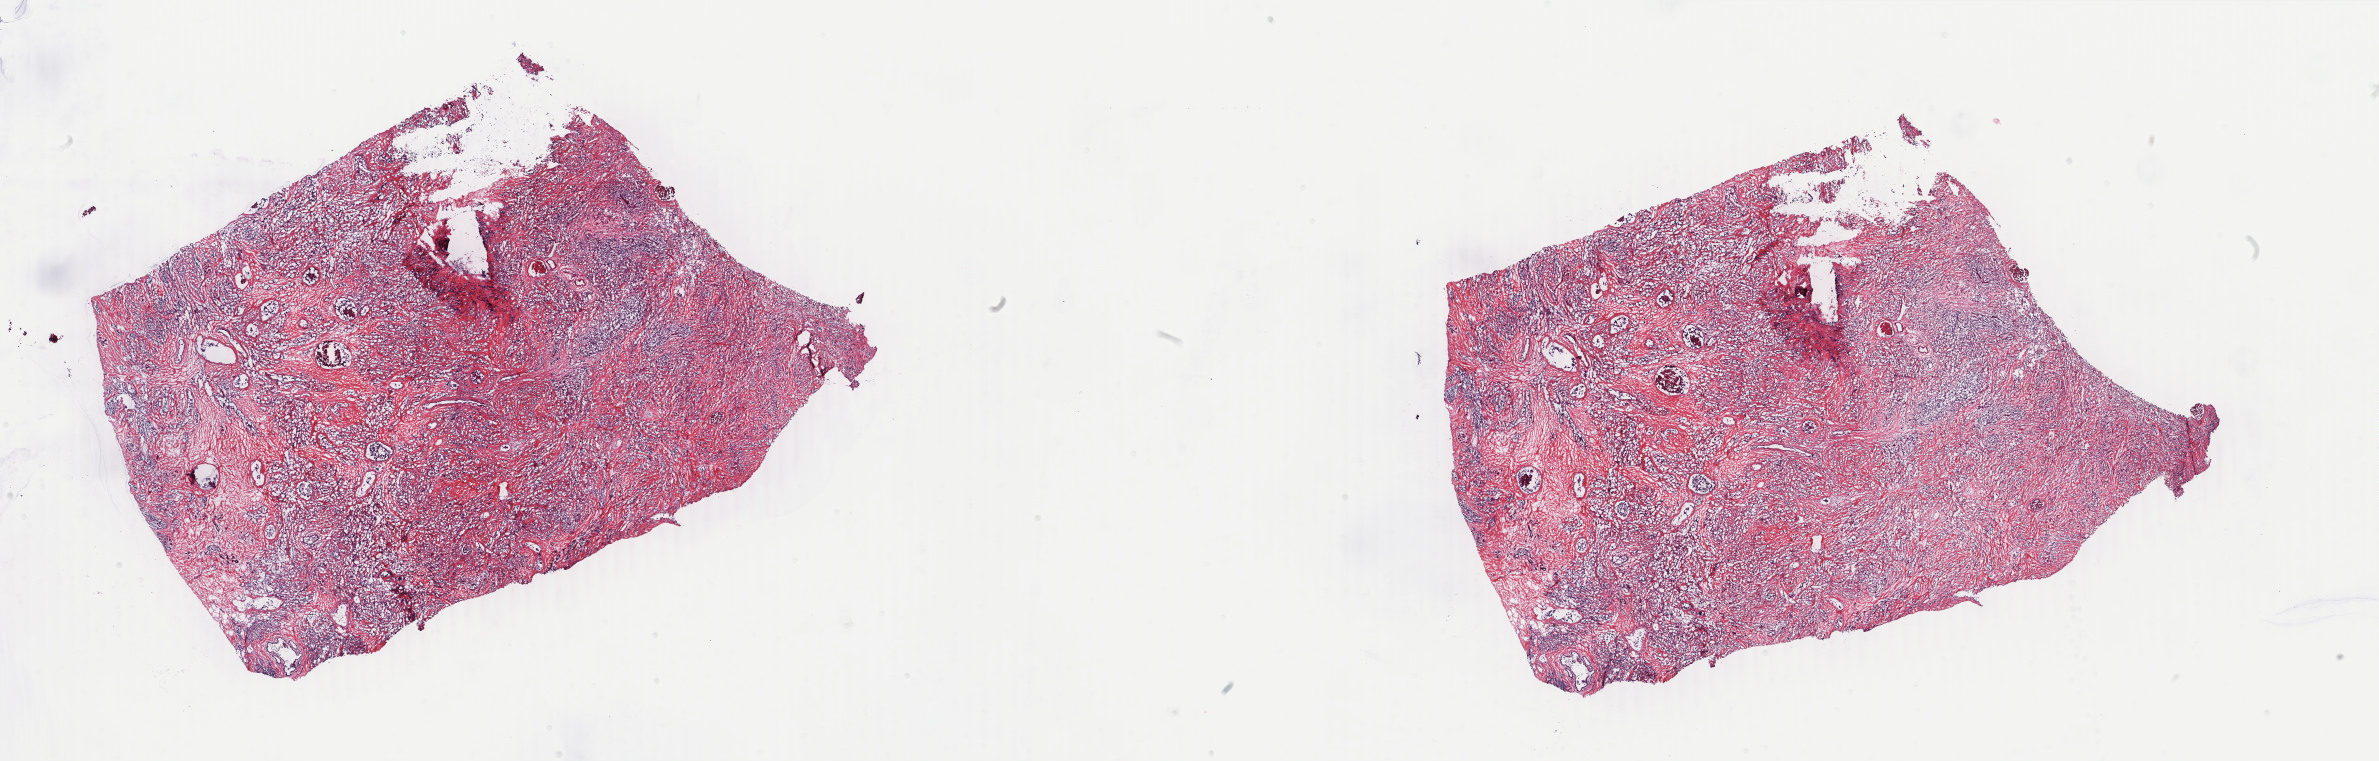
Whole-slide histology image, Hematoxylin and eosin (H&E) stained — low-resolution overview of the scanned area, about 37.8 x 12.1 mm. Frozen section from the top of the tissue portion. Primary tumour sample from the breast. Female, age 50 years at initial diagnosis. Pathologist review of this section (percent, as recorded): tumour cells 80%, tumour nuclei 80%.
Histologic diagnosis: Infiltrating duct carcinoma, NOS.